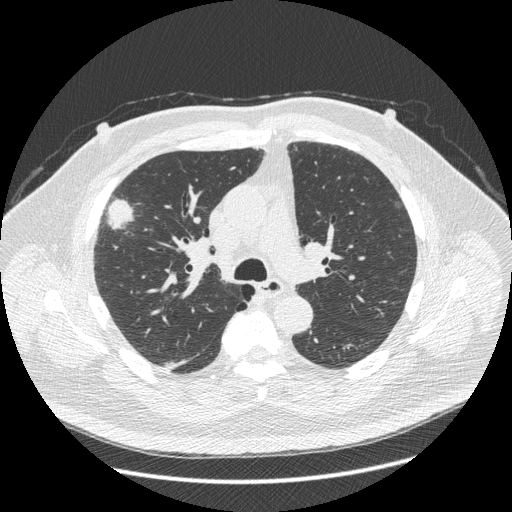
Low-dose screening chest CT, one axial slice. Slice 276 of 426 in the series (ordered by position). Reconstruction kernel STANDARD. Lung window (W 1500 / L -600 HU). 1.25 mm slice thickness. 512 × 512 image matrix.
Annotated regions visible in this slice (expert manual segmentation):
- lesion 1 (tumor, upper lobe of right lung): bounding box [x1, y1, x2, y2] px = [108, 199, 133, 228]